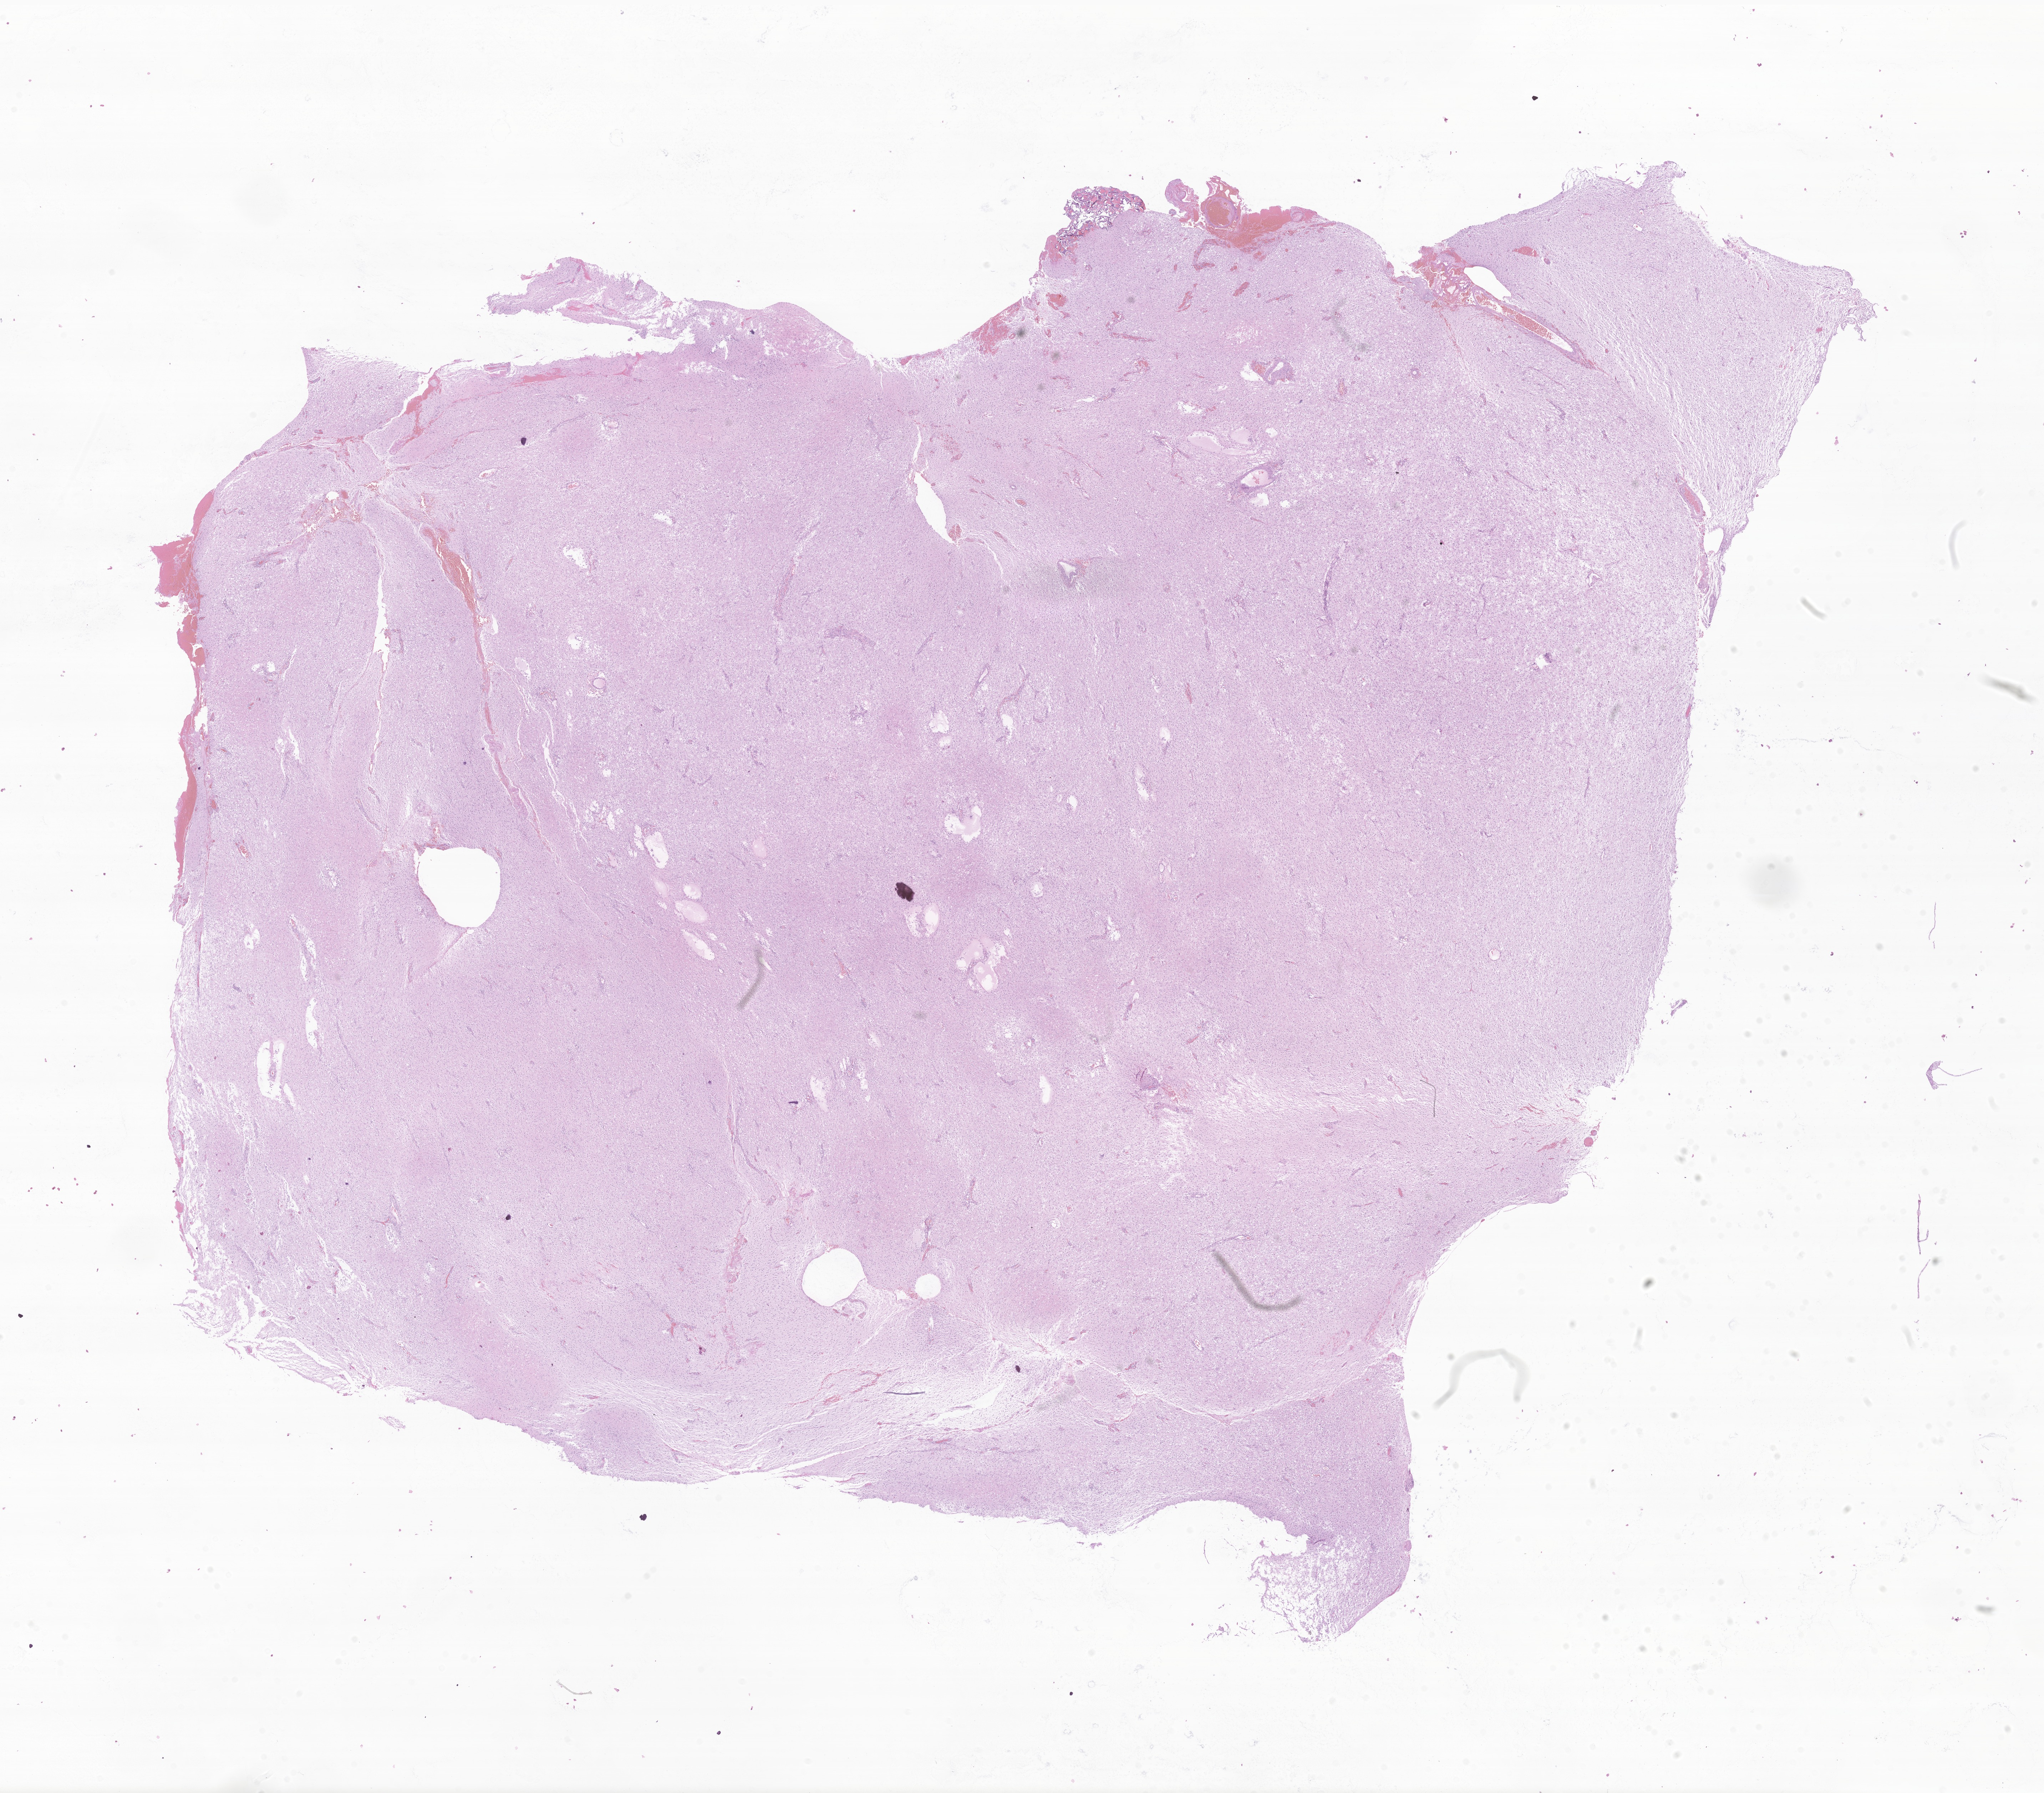
Digitized H&E-stained section of tumor tissue from the brain — low-resolution overview of the scanned area, about 24.2 x 21.2 mm. Formalin-fixed, paraffin-embedded (FFPE) tissue. Patient: female, age 117 months (9 years 9 months).
Diagnosis: Pilocytic astrocytoma.